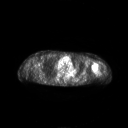
FDG PET of an extremity soft-tissue mass (from a PET/CT study), one axial slice. Slice 184 of 267 in the series (ordered by position). 3.27 mm slice thickness. 128 × 128 image matrix. Female patient, age 83 years. Case-level facts recorded for this patient, not image findings: histological type: pleiomorphic leiomyosarcoma; grade: high; site of the primary tumour: left biceps.
Outlined on this slice (expert contour drawn on MRI and transferred to this co-registered scan by the dataset authors):
- gross tumour volume including surrounding oedema: bounding box <91,63,98,73> (left, top, right, bottom; pixels)
- gross tumour volume (mass): <91,64,97,70>